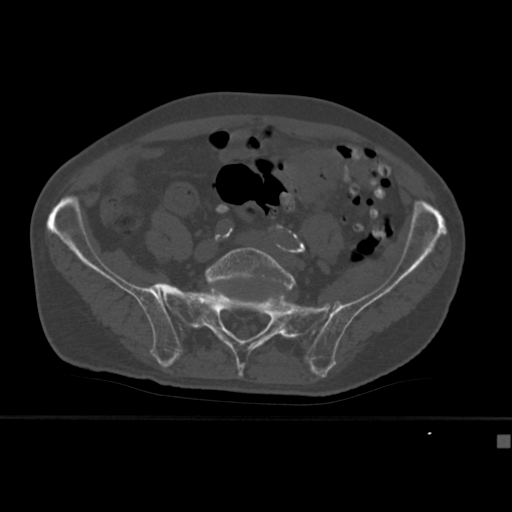
CT including the spine, one axial slice; slice 75 of 430 in the series (ordered by position); reconstruction kernel Br40s; 120 kVp; bone window (W 1800 / L 400 HU); 512 × 512 image matrix. Male patient, age 64 years. Case-level facts recorded for this patient, not image findings: primary cancer: uterus; vertebrae with lytic lesions (as recorded): T1, T4, T5, T7, L5.
Outlined on this slice (semi-automatic segmentation, software-assisted and operator-edited):
- L5 vertebra: box from (x=206, y=247) to (x=296, y=291) px